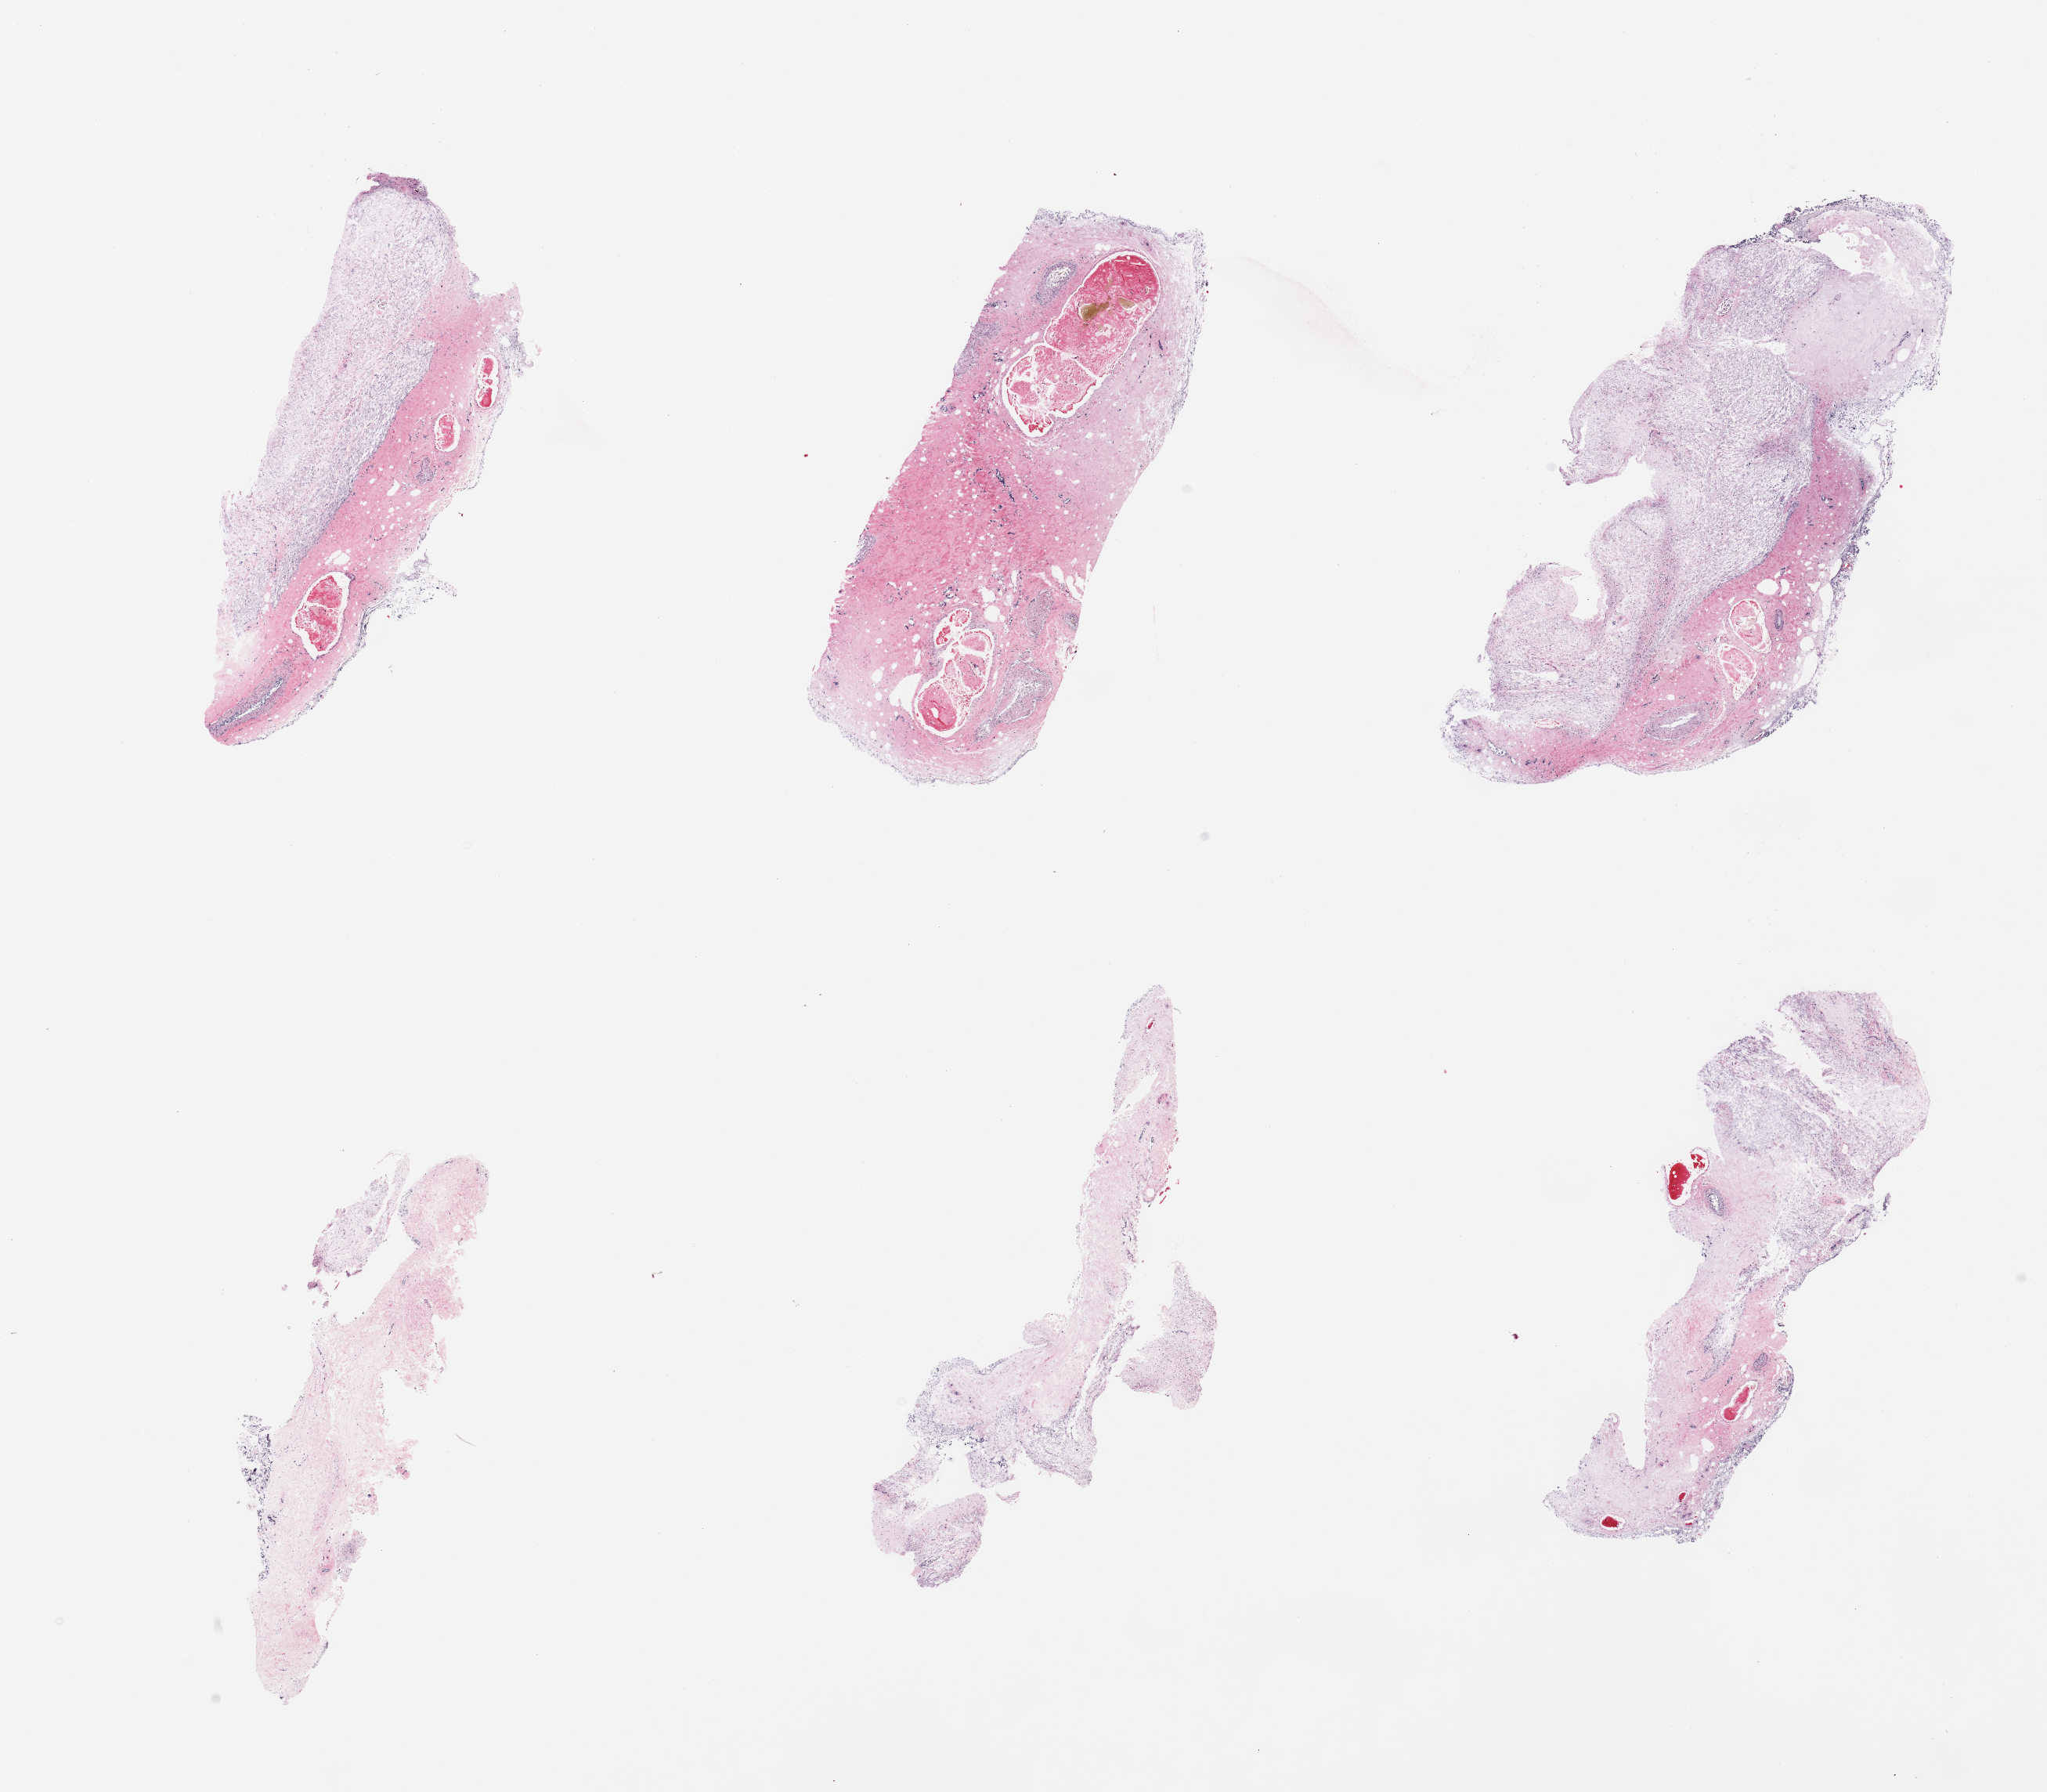
Whole-slide image, hematoxylin and eosin (H&E) stain, brightfield, whole scanned area (about 20.7 x 18.1 mm, from a 20x scan) shown as a low-resolution overview, PAXgene-fixed, paraffin-embedded tissue, section of stomach (target tissue), tissue donor sample. Donor sex: male.
- review note (as recorded): 6 pieces;mucosa too autolyzed for further study; no muscularis